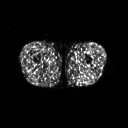
FDG PET of an extremity soft-tissue mass (from a PET/CT study), one axial slice; position 221 of 267 along the scan axis; 3.27 mm slice thickness; 128 × 128 image matrix, field of view 500 × 500 mm. Patient: male, 27 years. Case-level facts recorded for this patient, not image findings: histological type: extraskeletal osteosarcoma; grade: high; site of the primary tumour: left adductur.
Outlined on this slice (expert contour drawn on MRI and transferred to this co-registered scan by the dataset authors):
- gross tumour volume (mass): box from (x=70, y=62) to (x=90, y=70) px